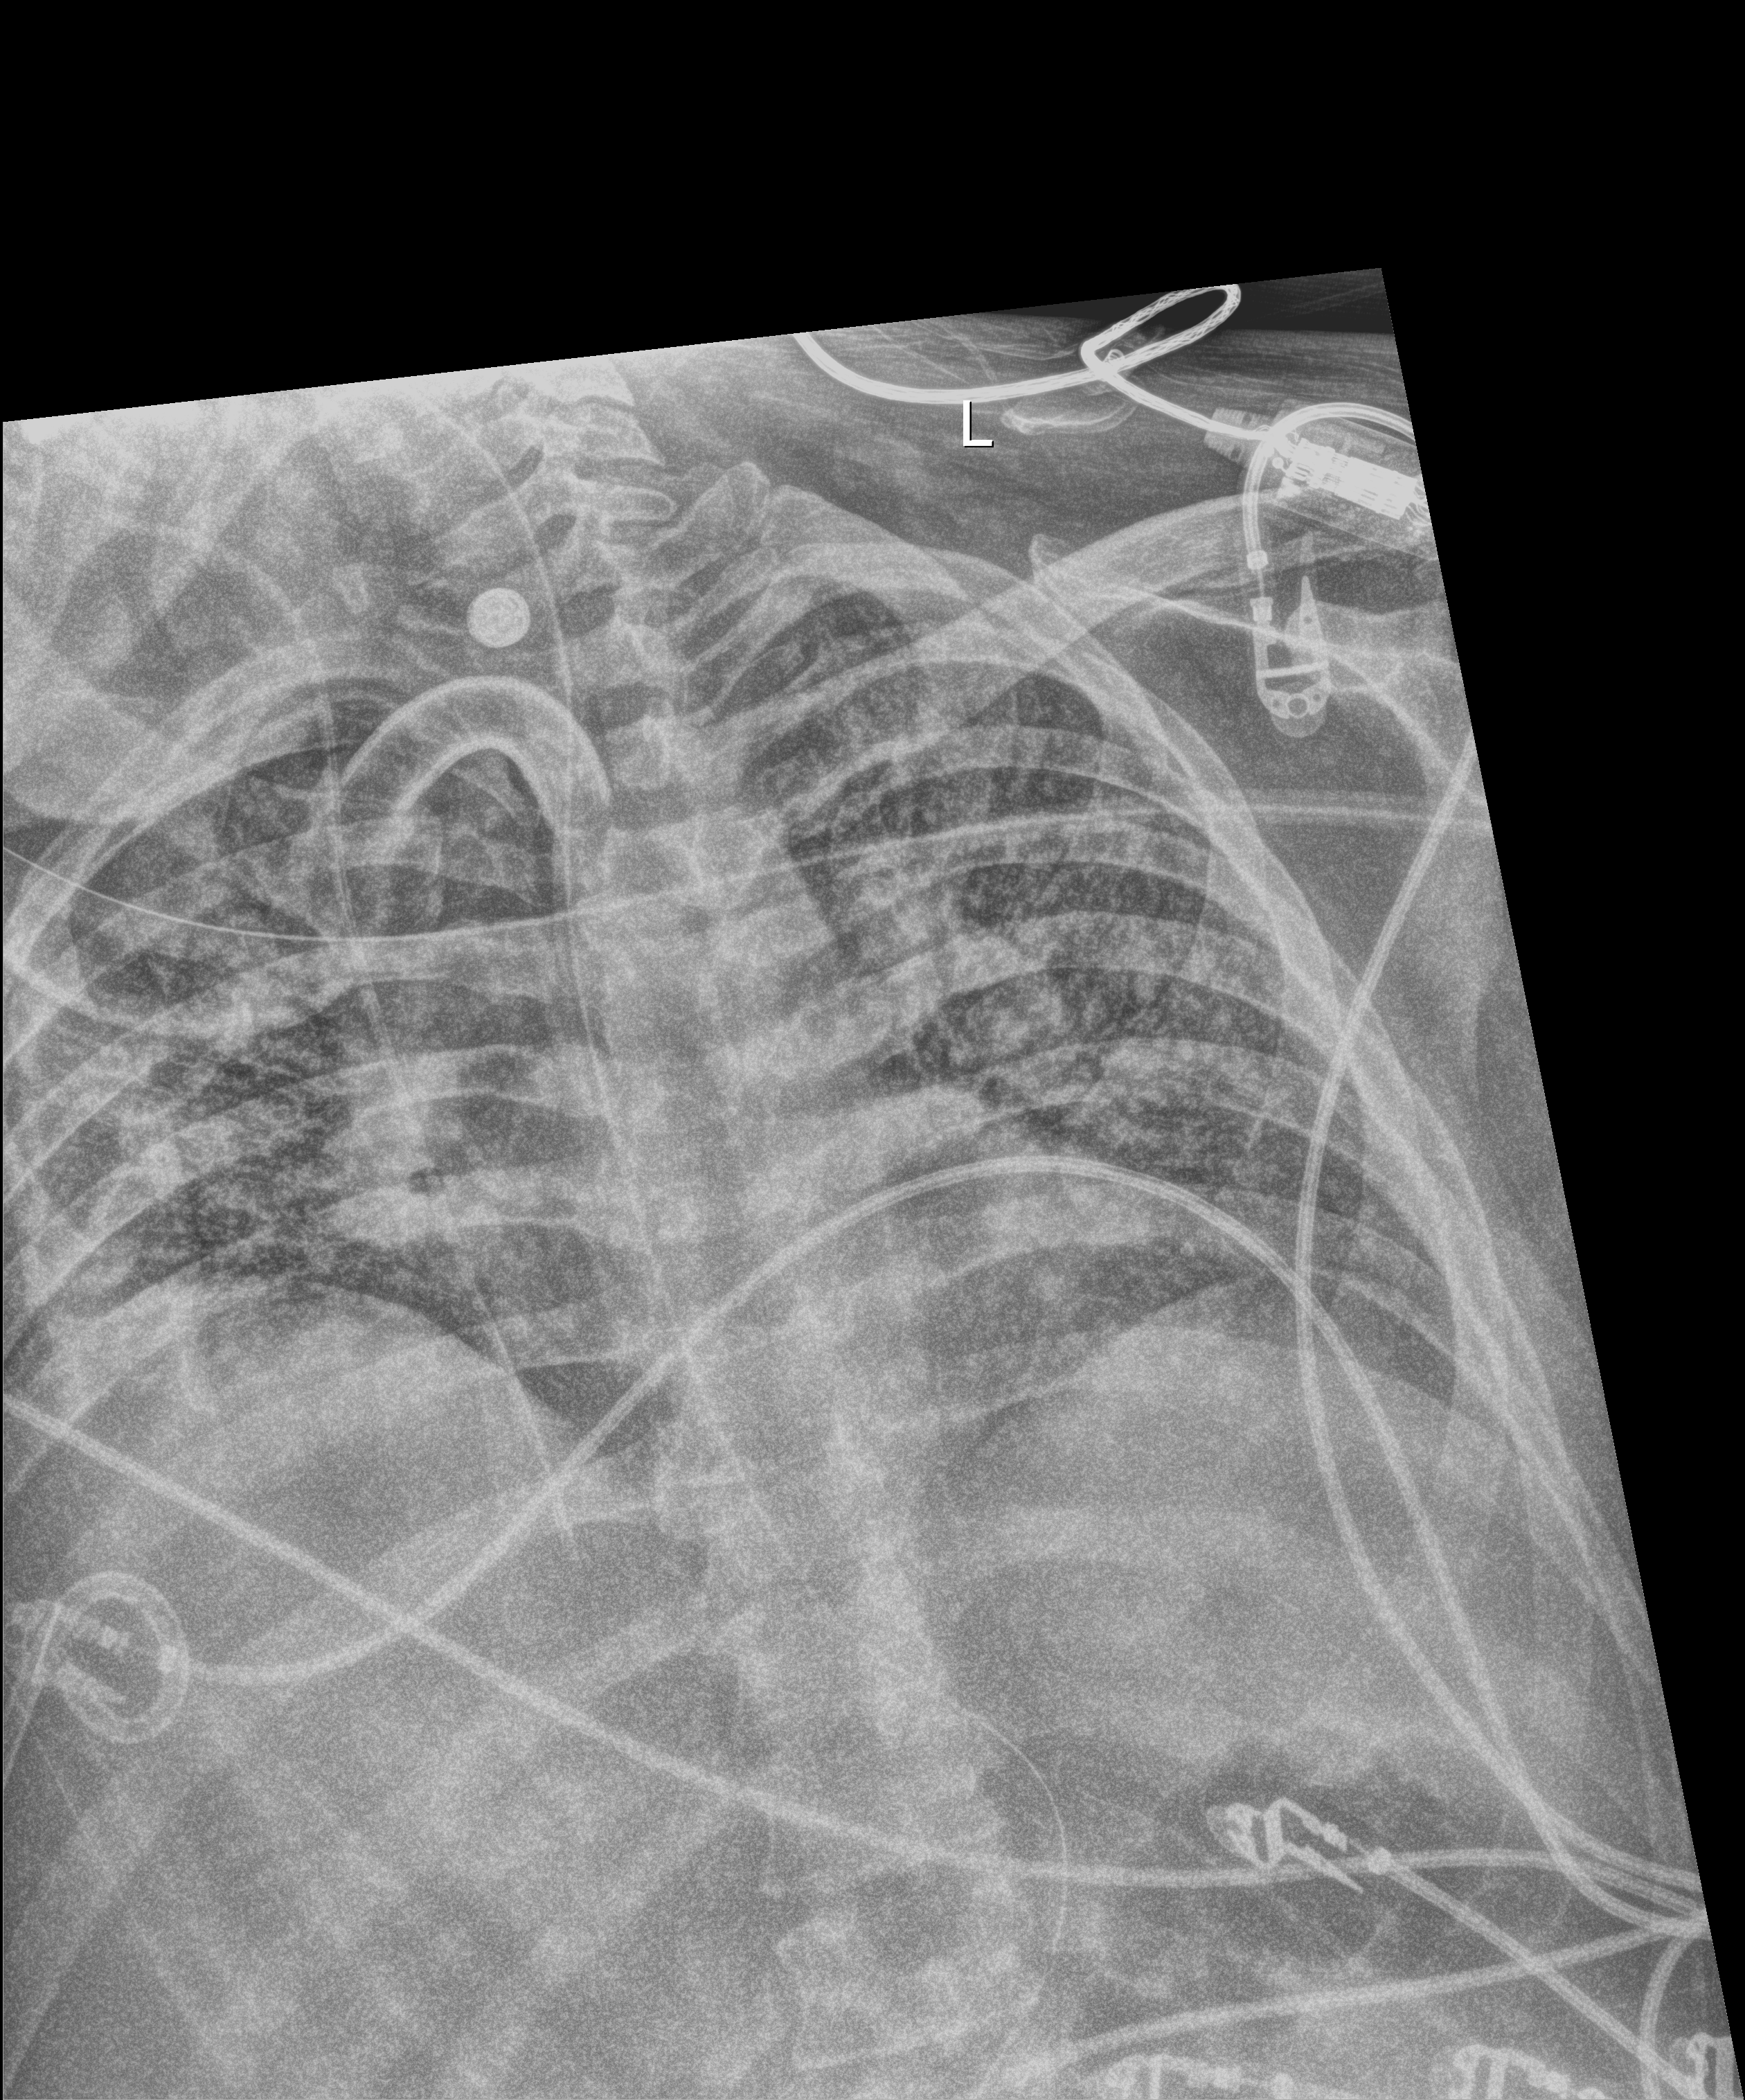
Portable chest radiograph. Patient hospitalised with COVID-19; male, aged 18–59 years.
From the hospital-stay record, not from the radiograph (when in the stay this image was taken is not recorded): mechanically ventilated during this hospital stay: yes; admitted to intensive care during this hospital stay: yes; other chronic lung disease (admission record): no.